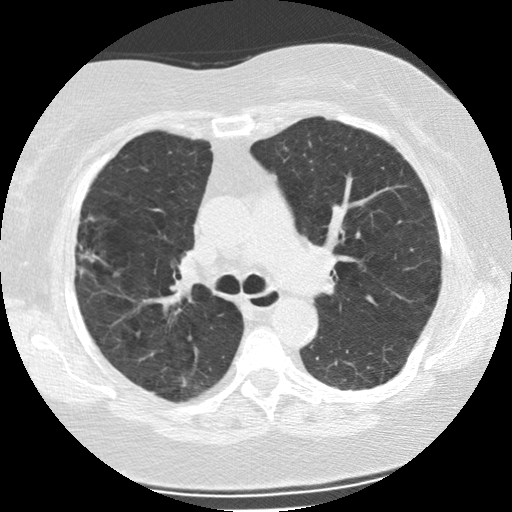
Low-dose screening chest CT, one axial slice; position 148 of 225 along the scan axis; 120 kVp; lung window (W 1500 / L -600 HU); 2.5 mm slice thickness; 512 × 512 image matrix, field of view 320 × 320 mm.
Outlined on this slice (manually delineated by an expert):
- lesion 1 (tumor, upper lobe of right lung): bounding box (x1, y1, x2, y2) in pixels: (82, 253, 96, 262)